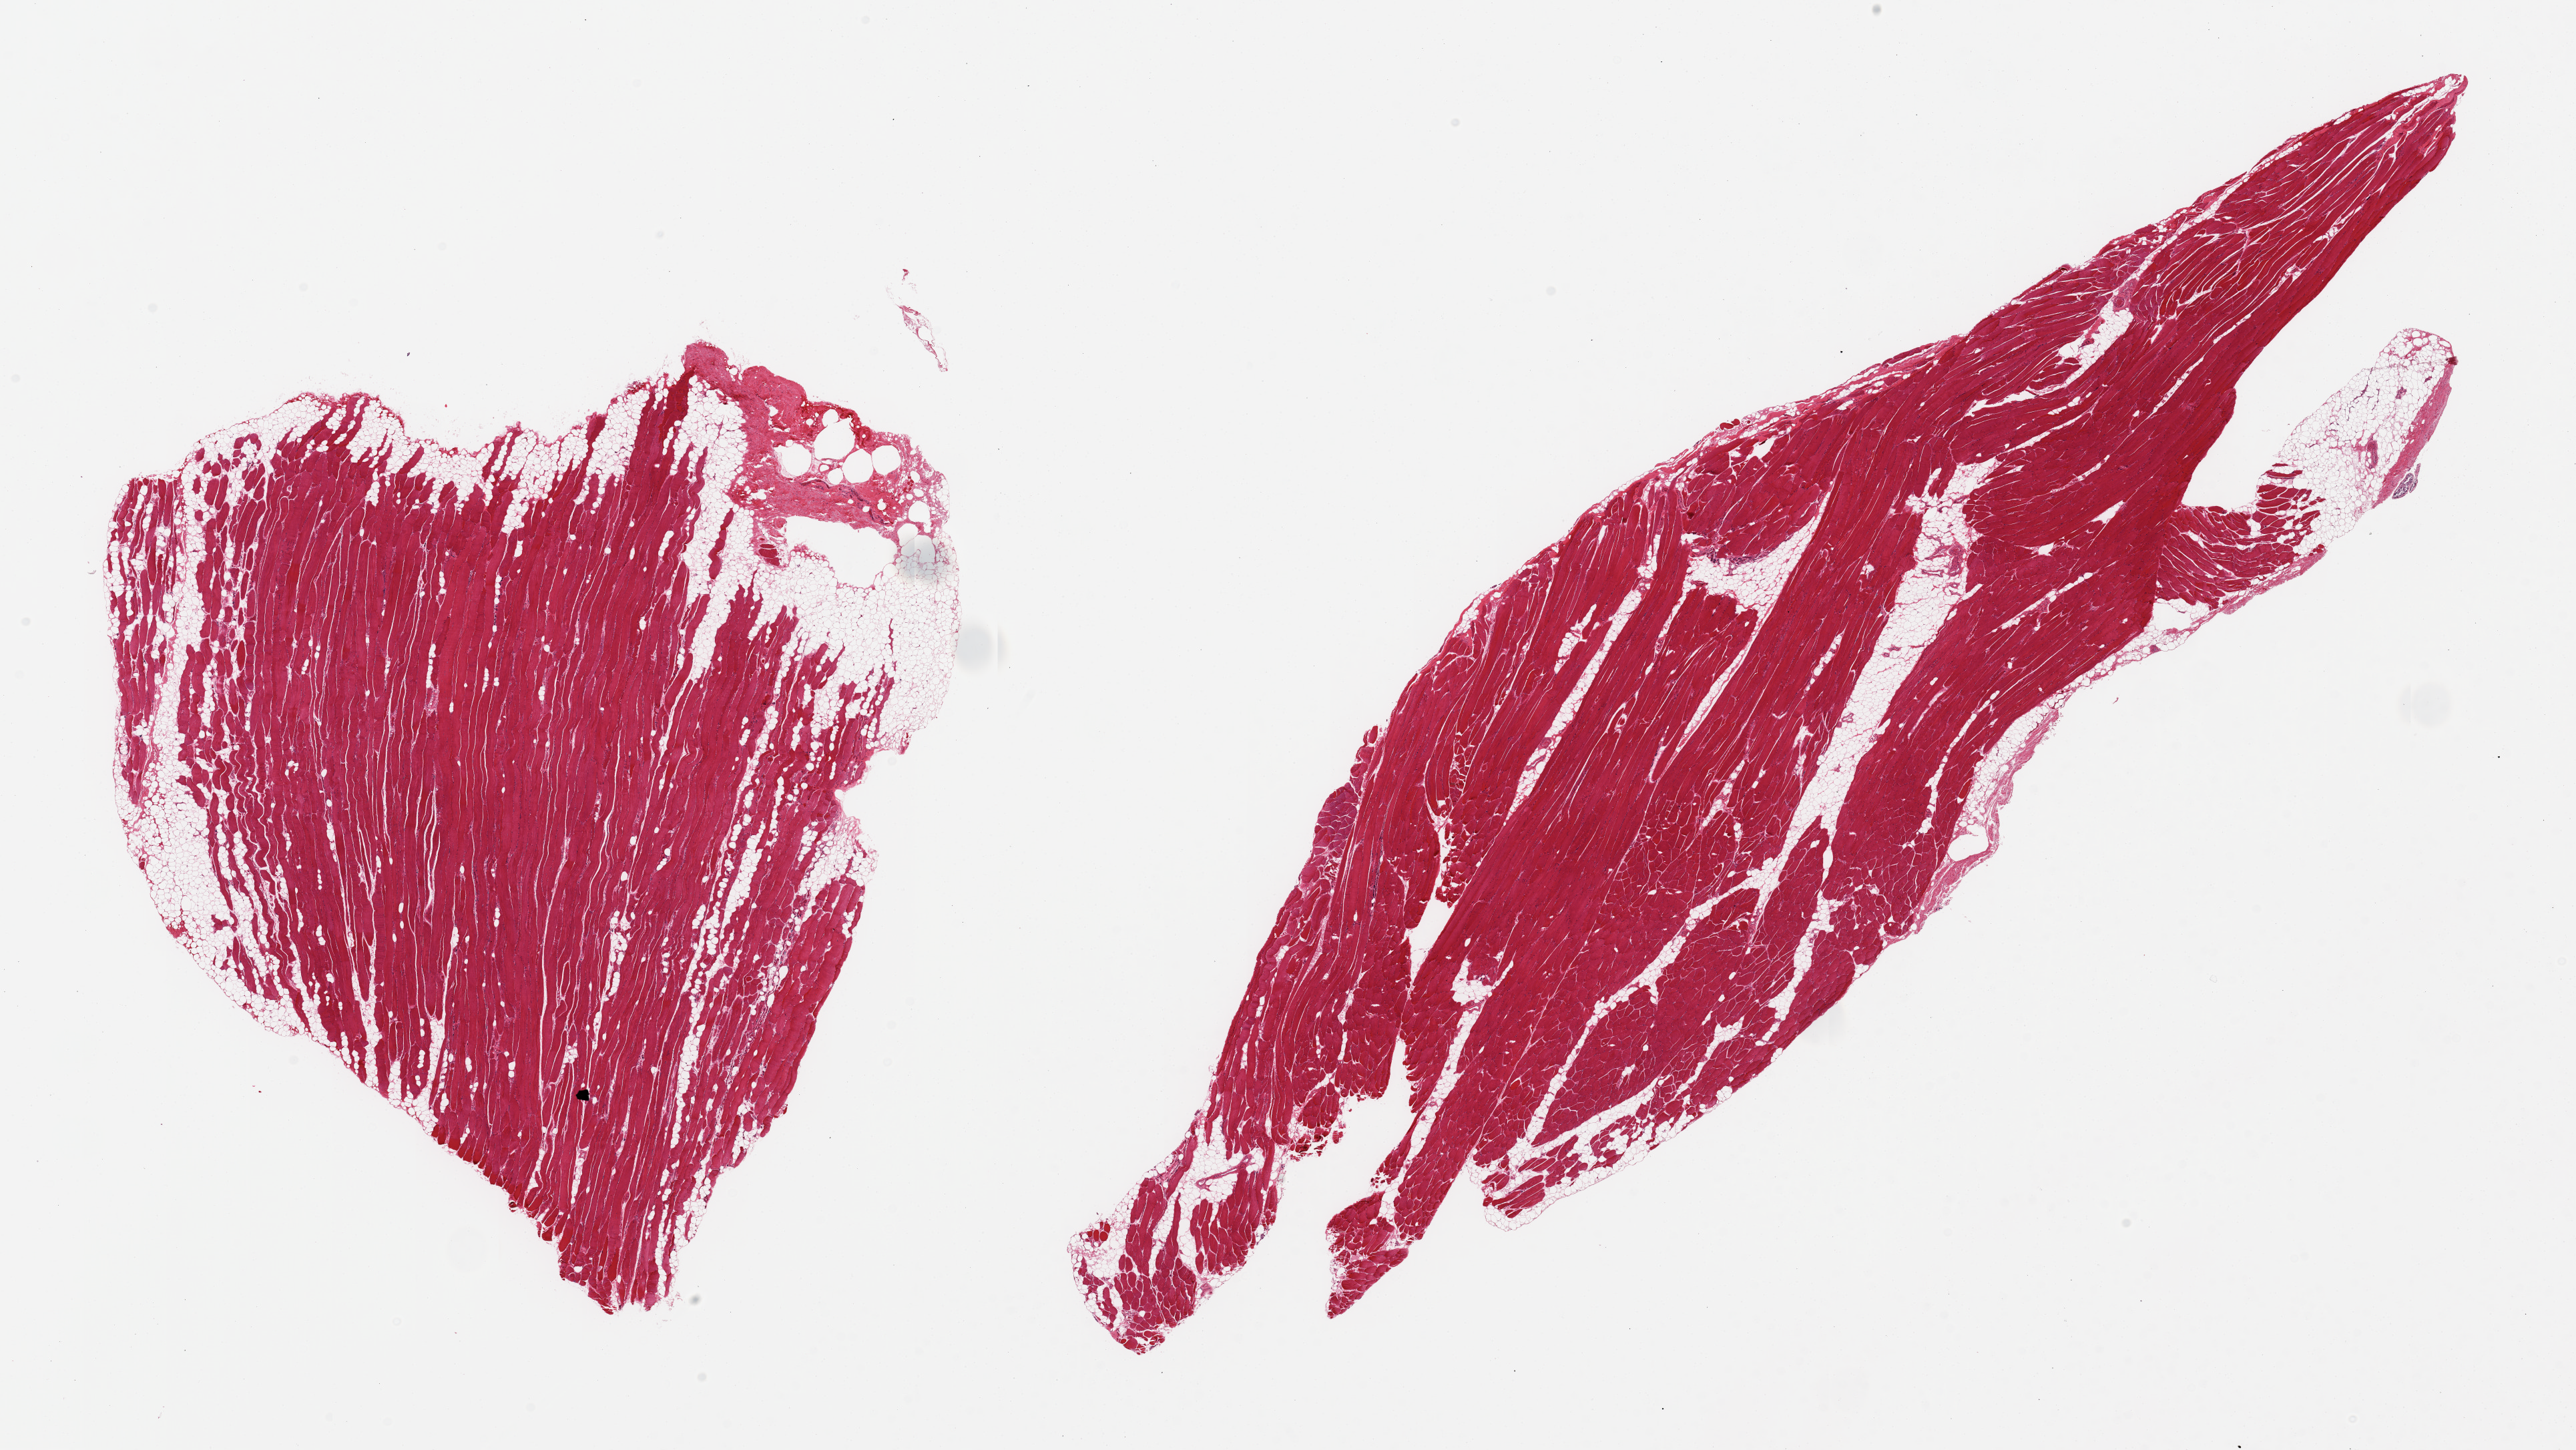
Haematoxylin and eosin whole-slide image, whole scanned area (about 30.5 x 17.2 mm, from a 20x scan) shown as a low-resolution overview. PAXgene-fixed, paraffin-embedded tissue. Target tissue: skeletal muscle. Donor tissue sample. Male donor.
Pathologist's review note for this sample: 2 pieces; 20% and 10% internal fat.